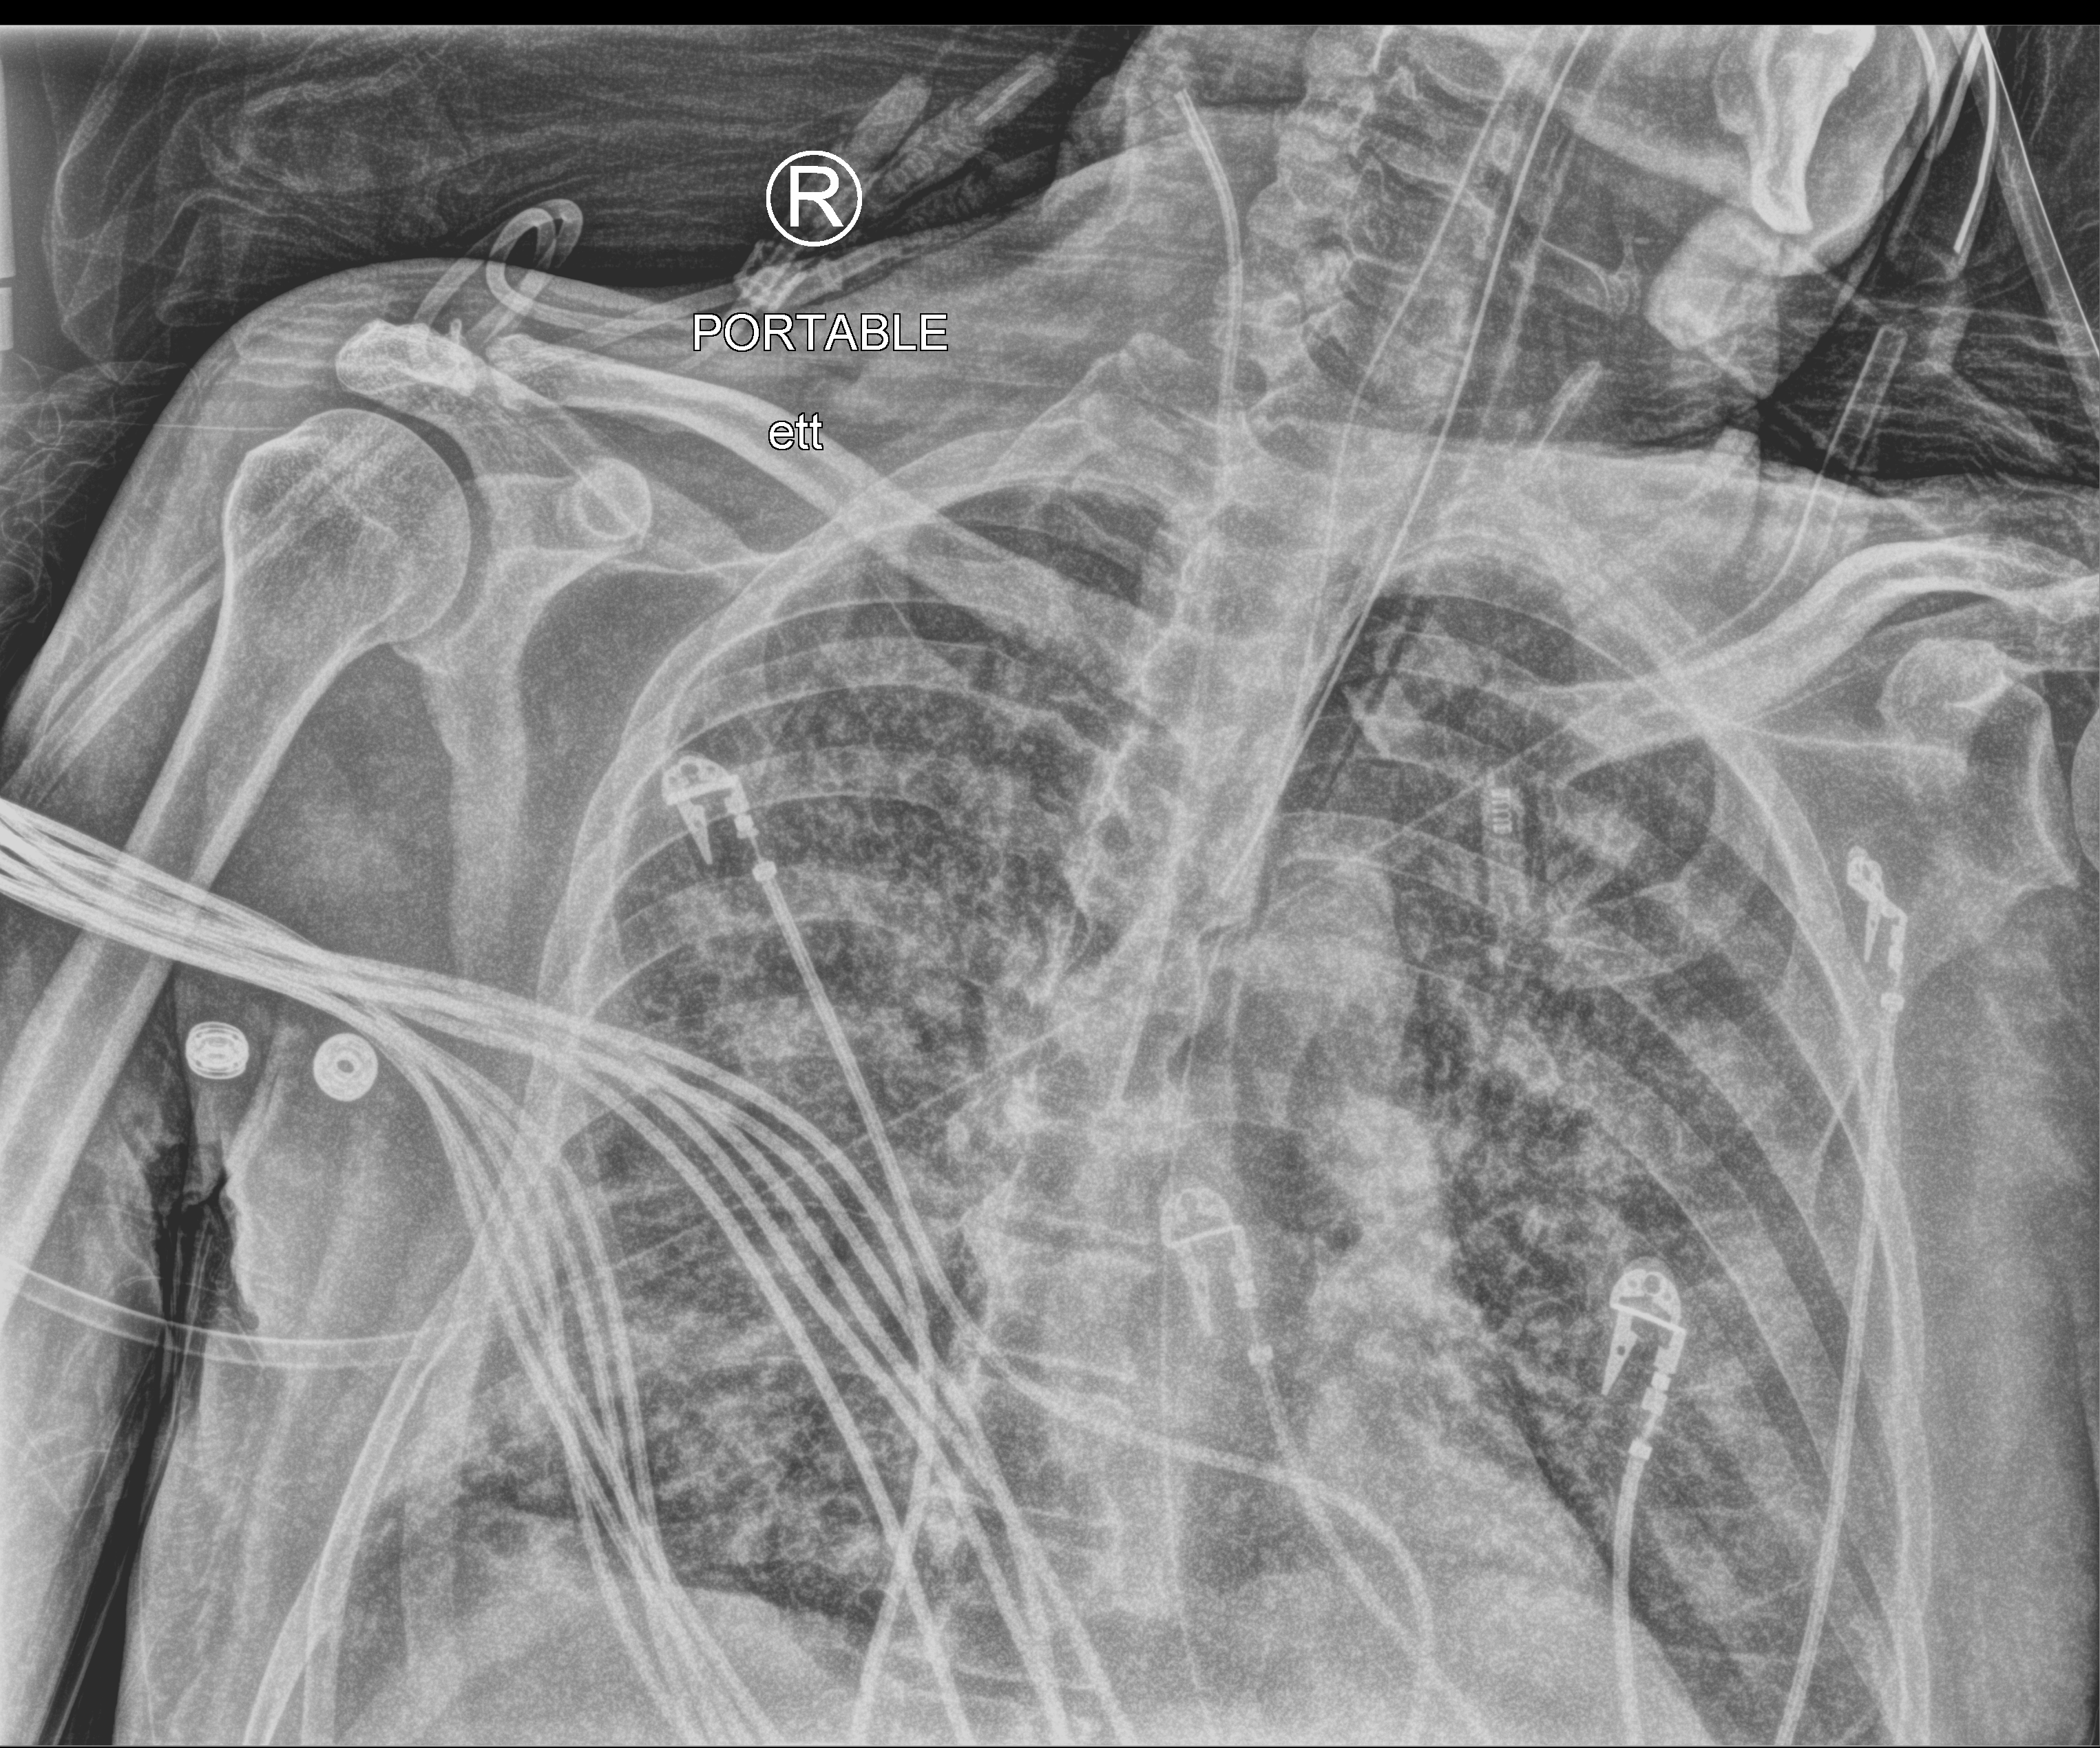
Portable chest radiograph, anteroposterior (AP) projection. Male patient hospitalised with COVID-19, age 60–74 years.
Hospital-stay facts (about this admission, not read from this image; timing relative to this image not recorded): admitted to intensive care during this hospital stay: yes.